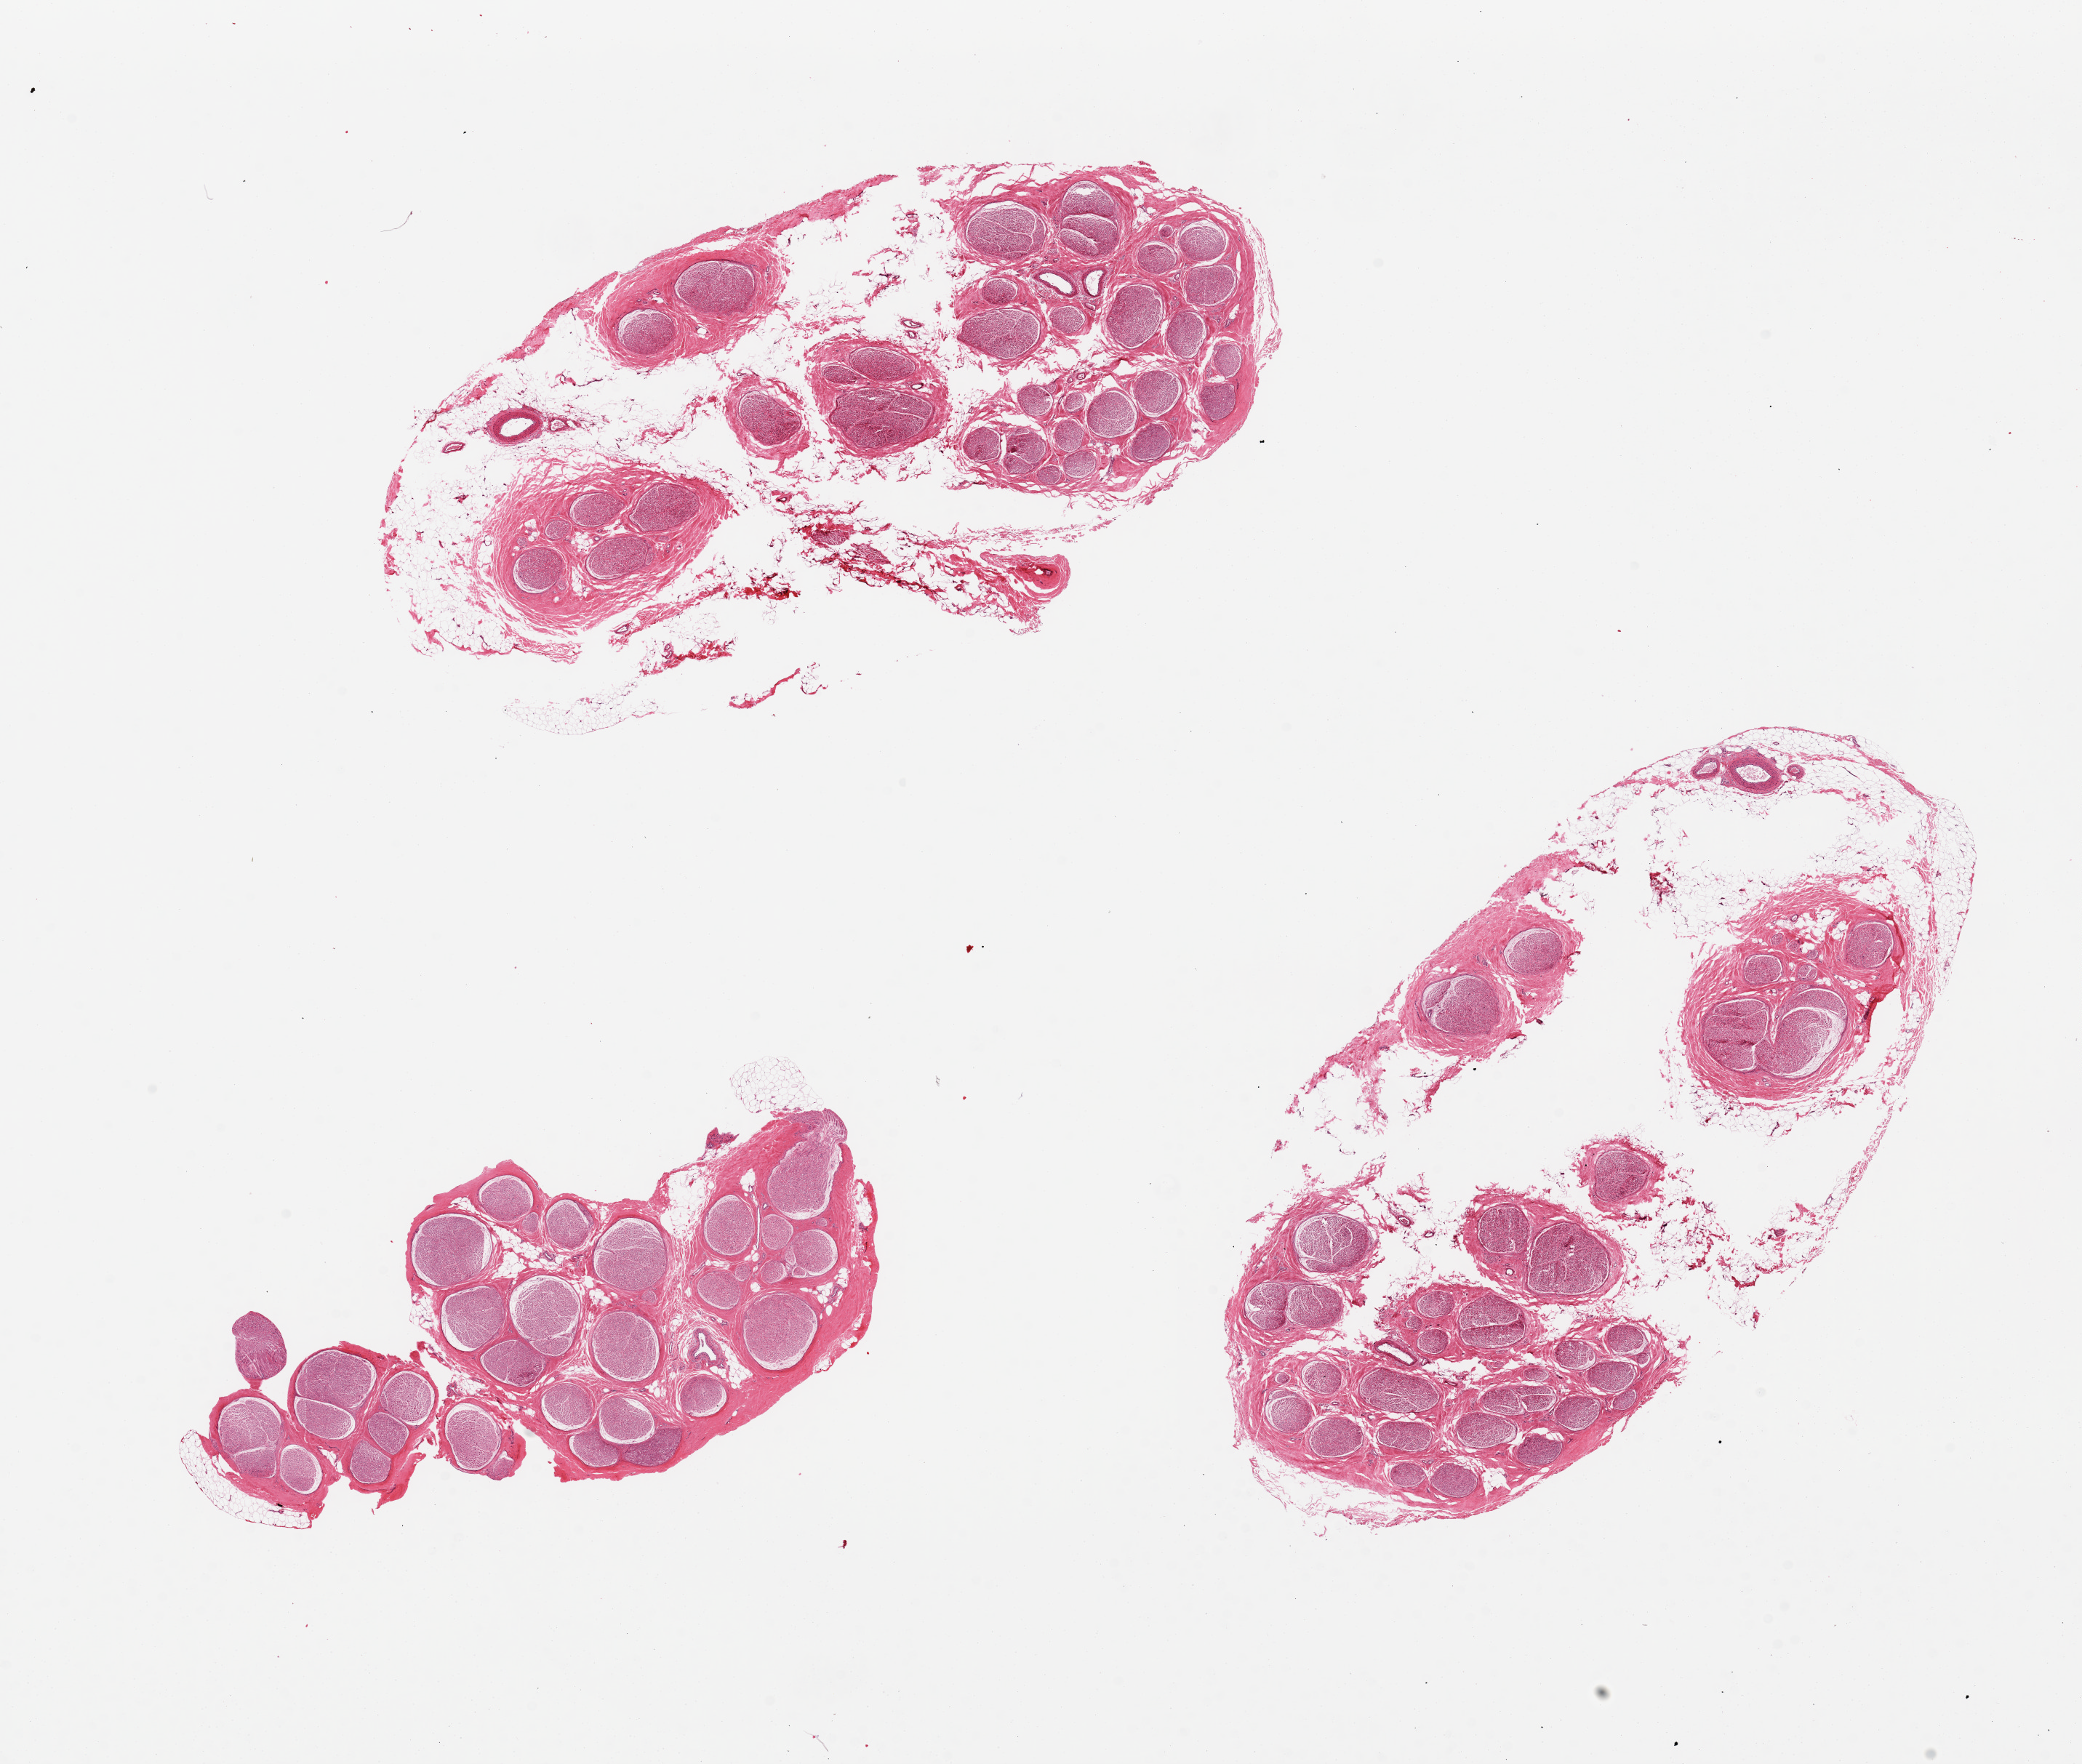
Whole-slide image, H&E stain — shown as a low-resolution overview of the whole scanned area (about 22.6 x 19.2 mm), PAXgene-fixed, paraffin-embedded tissue, sampled site (target tissue): tibial nerve, tissue donor sample. Donor: male.
Reviewer comment on this tissue sample: 3 pieces, larger 2 include up to 50% fat, not fully intact (? poor fixation).